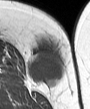
MRI of an extremity soft-tissue mass, one axial slice; slice 12 of 45 in the series (ordered by position); MR volume resampled by the dataset authors to the PET/CT grid (not the native acquisition matrix); 3.27 mm slice thickness; 90 × 109 image matrix. Female patient. From the clinical record (not read from this slice): histological type: leiomyosarcoma; grade: intermediate; site of the primary tumour: parascapusular.
Structures marked on this image (expert contour drawn on MRI and transferred to this co-registered scan by the dataset authors):
- gross tumour volume including surrounding oedema: bounding box [x1, y1, x2, y2] px = [28, 39, 64, 86]
- gross tumour volume (mass): [28, 48, 64, 83]